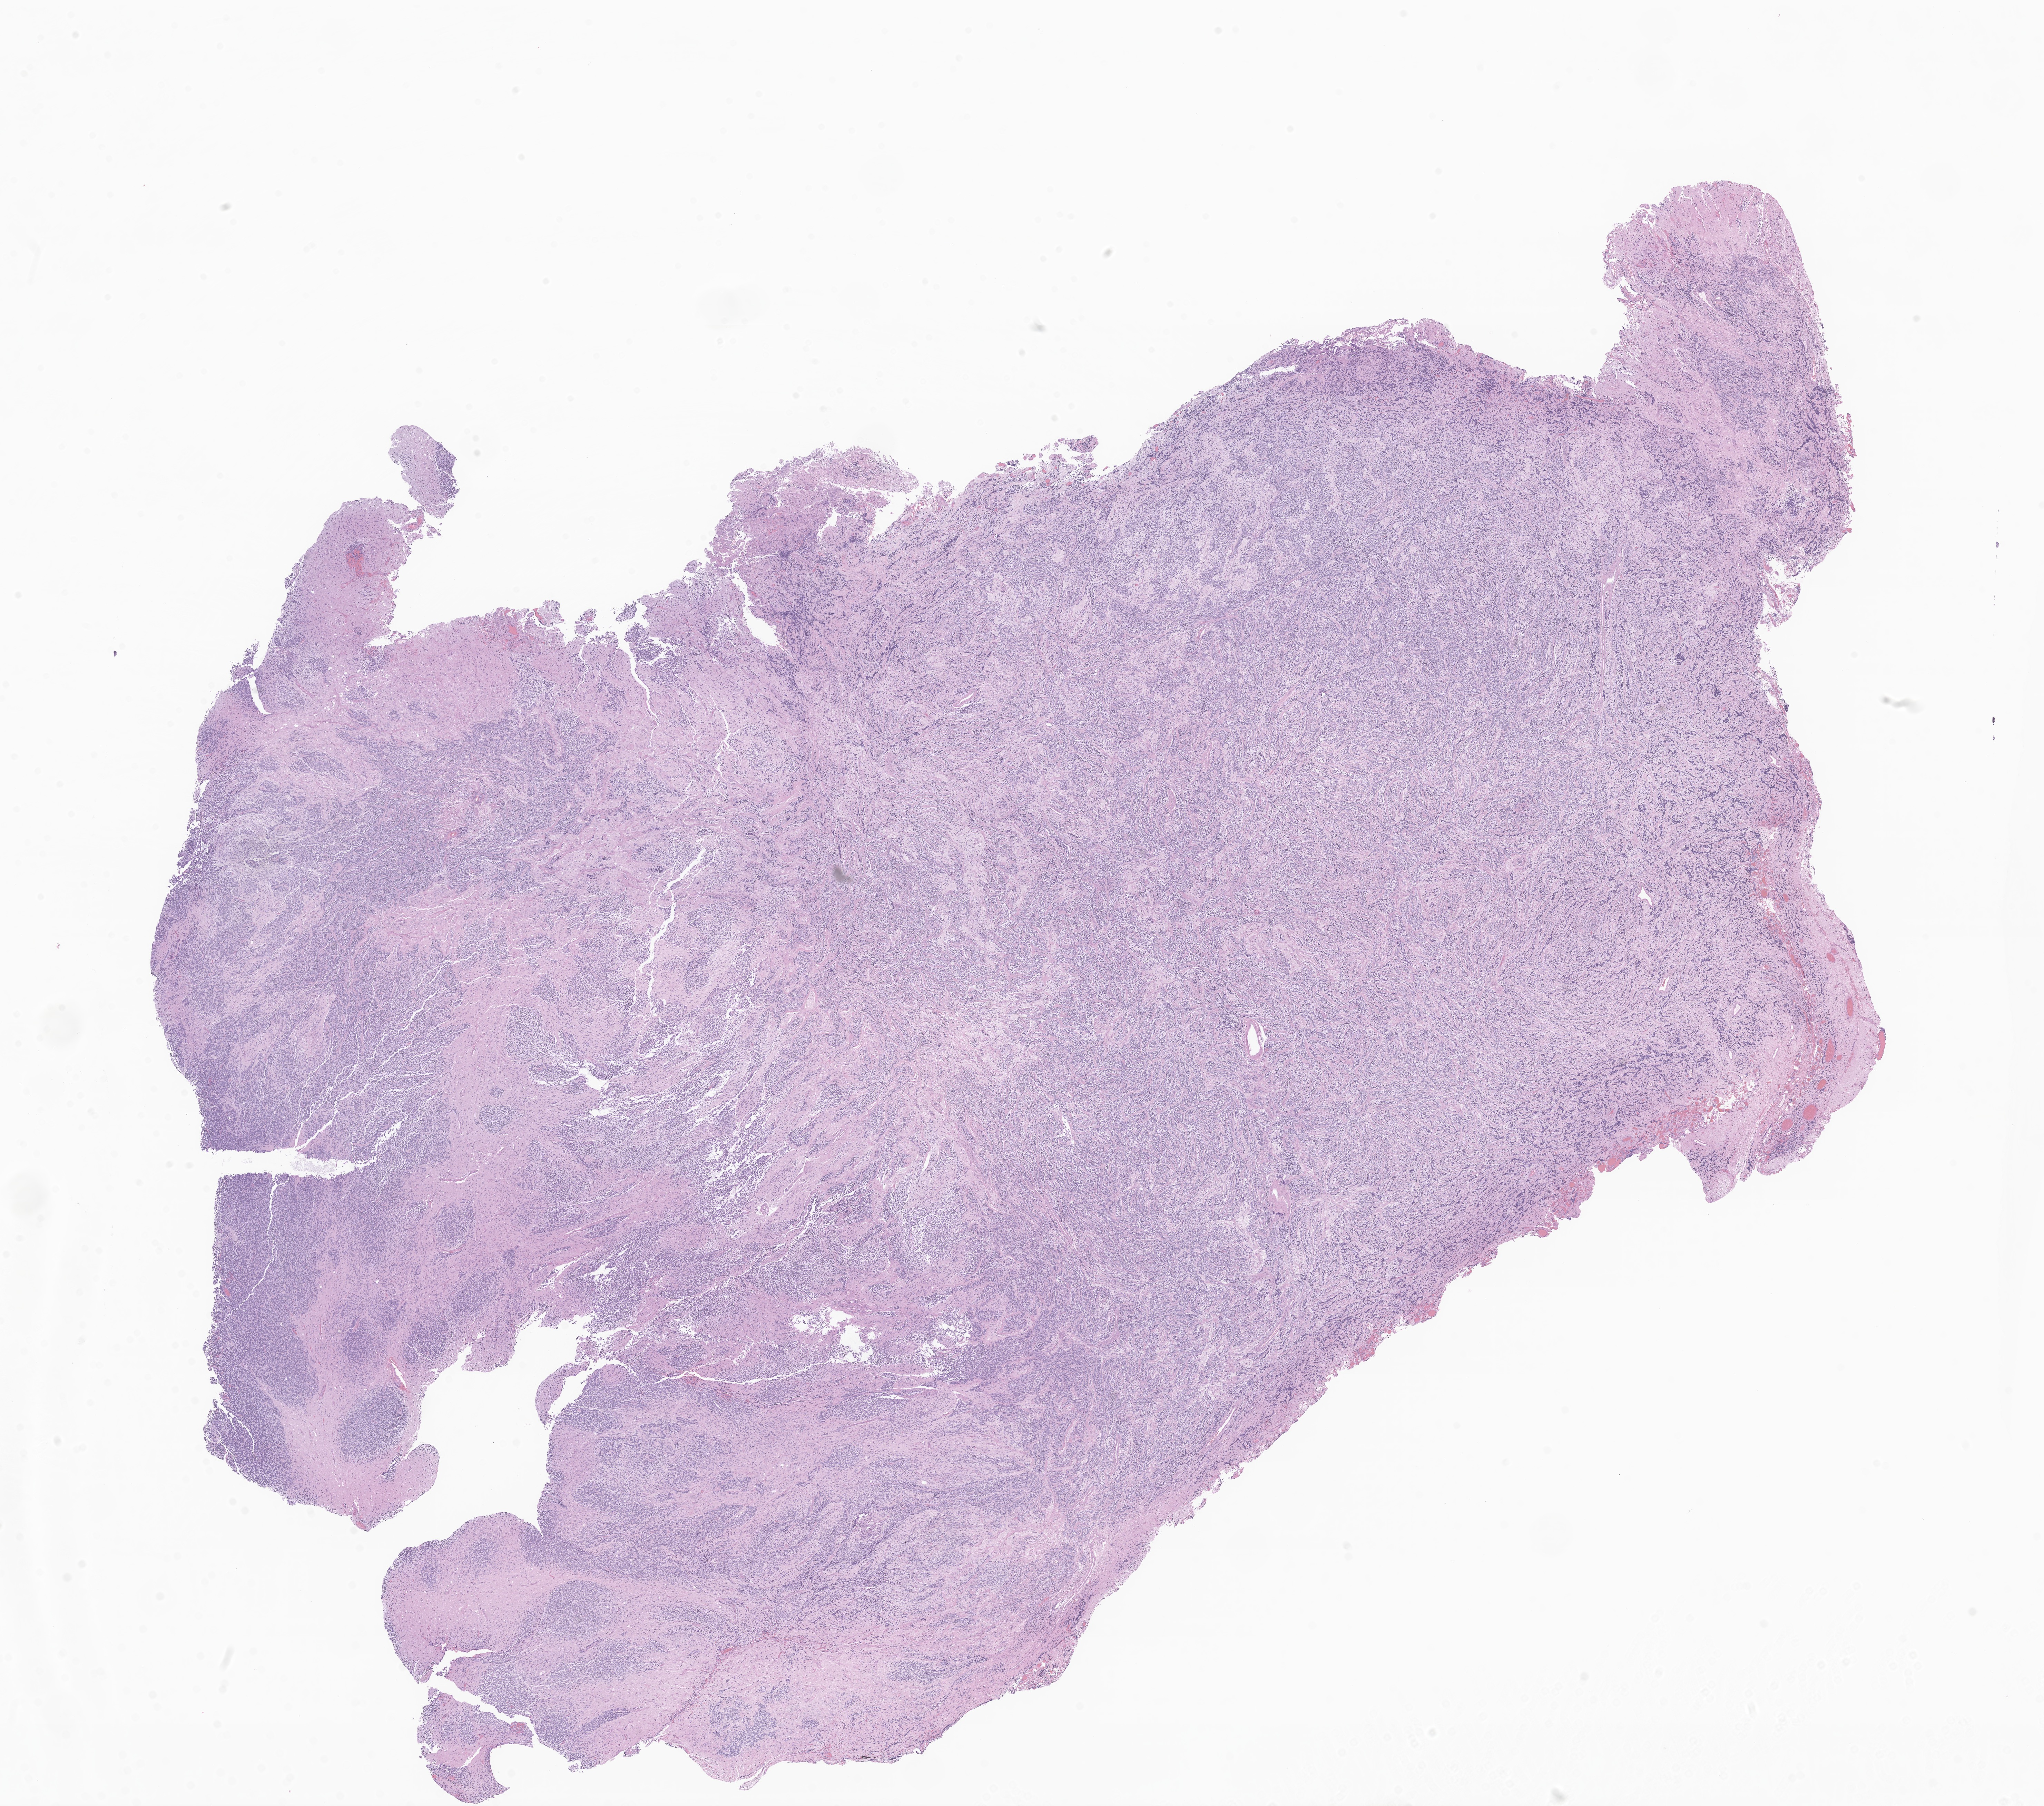
Digitized haematoxylin and eosin-stained section of tumor tissue from the brain, low-resolution overview of the scanned area, about 25.0 x 22.1 mm, formalin-fixed paraffin-embedded section. Male patient, age 90 months (7 years 6 months).
Diagnosis: Medulloblastoma, NOS.